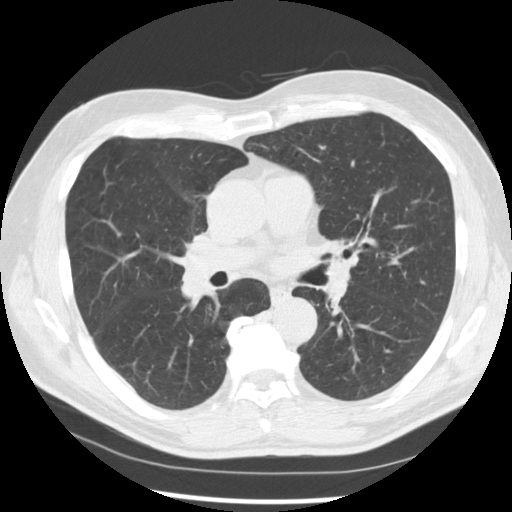
Low-dose screening chest CT, one axial slice; position 157 of 277 along the scan axis; reconstruction kernel STANDARD; lung window (W 1500 / L -600 HU); 2.5 mm slice thickness; 512 × 512 image matrix, field of view 365 × 365 mm.
Structures marked on this image (expert manual segmentation):
- lesion 1 (tumor, middle lobe of right lung): bounding box [x1, y1, x2, y2] px = [181, 266, 209, 303]